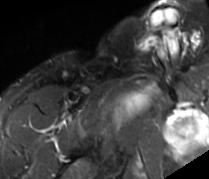
MRI of an extremity soft-tissue mass, one axial slice; position 77 of 89 along the scan axis; STIR; MR volume resampled by the dataset authors to the PET/CT grid (not the native acquisition matrix); 3.27 mm slice thickness; 209 × 179 image matrix. Male patient. From the clinical record (not read from this slice): histological type: undifferentiated - pleiomorphic; grade: high; site of the primary tumour: right thigh.
Outlined on this slice (expert contour drawn on MRI and transferred to this co-registered scan by the dataset authors):
- gross tumour volume including surrounding oedema: bounding box <108,84,159,124> (left, top, right, bottom; pixels)
- gross tumour volume (mass): <114,92,147,120>